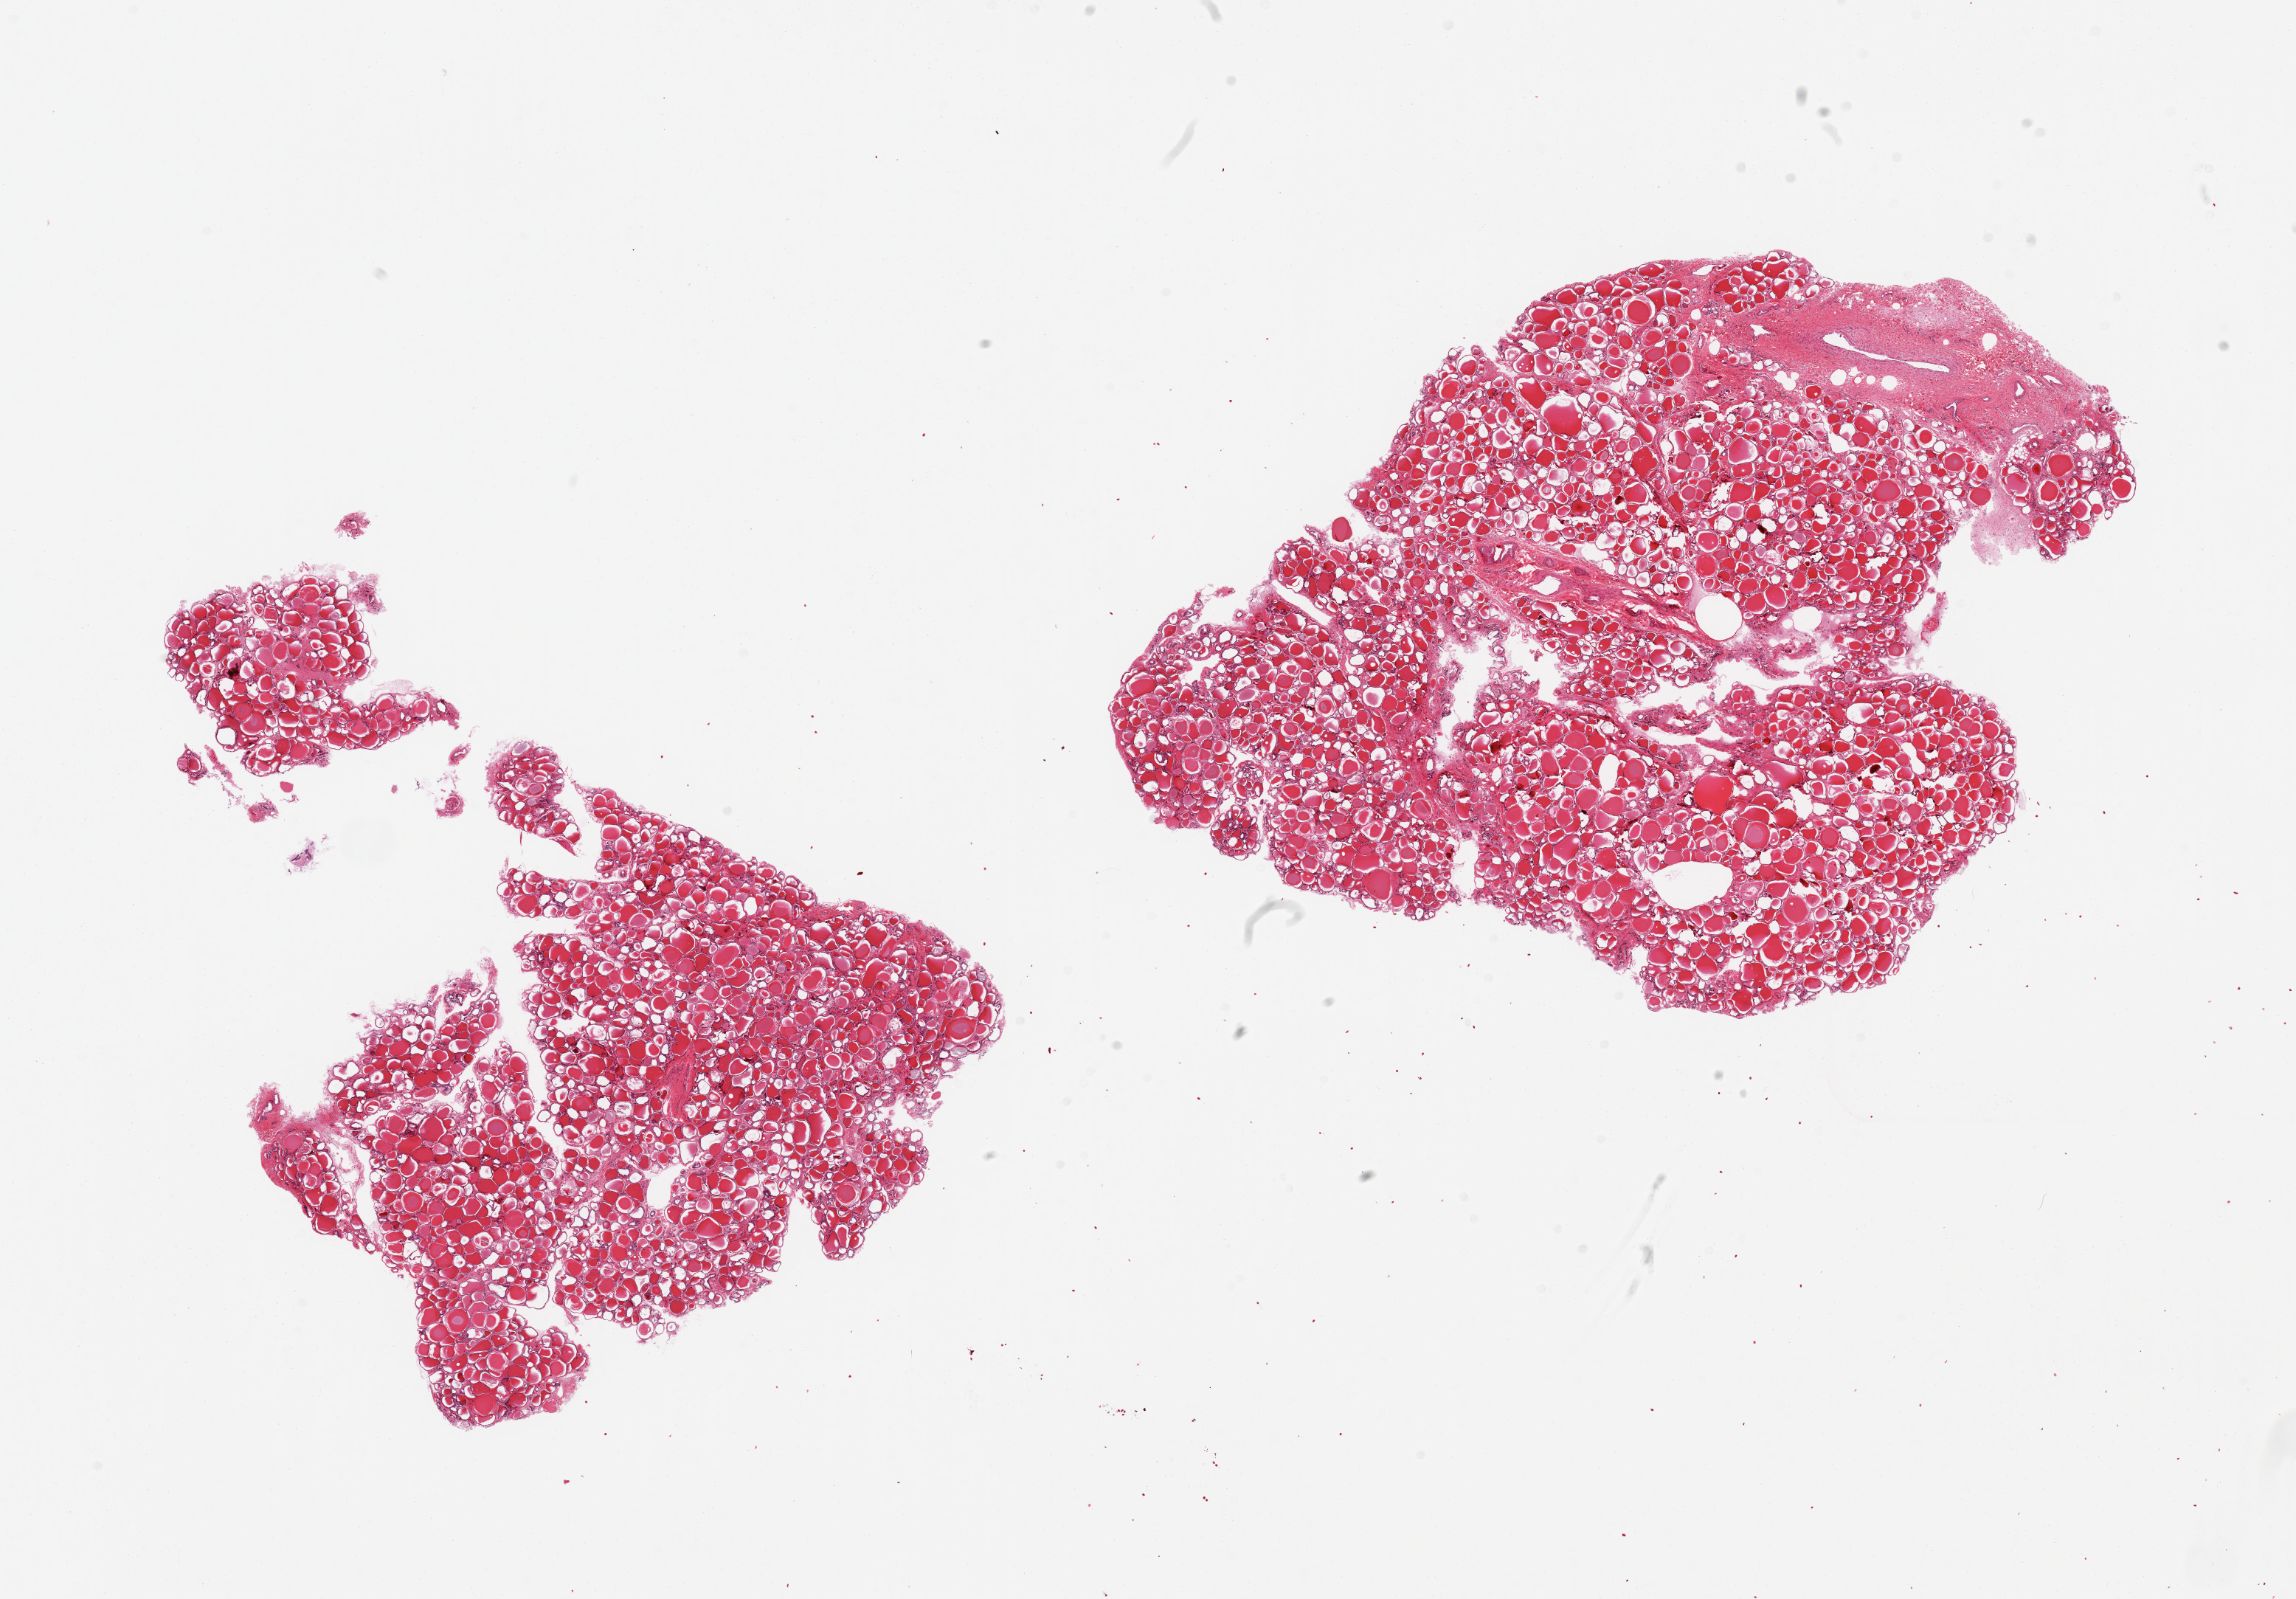
Whole-slide image, hematoxylin and eosin (H&E) stain, brightfield, low-resolution overview of the scanned area, about 24.6 x 17.1 mm; PAXgene-fixed paraffin-embedded (PFPE) section; target tissue: thyroid; tissue donor sample. Male donor.
* pathologist's review note for this sample: 2 pieces